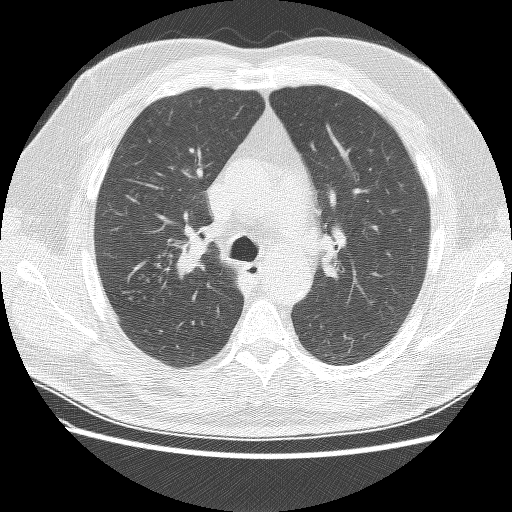
Chest CT (low-dose screening protocol), one axial image, first (baseline) screen, lung window (W 1500 / L -600 HU), 2.5 mm slice thickness, slice 62 of 159 in the series. Male, age 57 years at enrolment. Current smoker at enrolment.
- Expert reader's lesion annotation, bounding box [x1, y1, x2, y2] px = [158, 240, 213, 294].
- No non-calcified nodule or mass ≥4 mm was recorded by the screening reader at this exam.
- Official screen result: negative screen, minor abnormalities not suspicious for lung cancer.
- Lung cancer was diagnosed 434 days after this screen (after the second annual screen): non-small cell carcinoma, right upper lobe, poorly differentiated (G3), stage IIA (AJCC 6th edition), 25 mm at pathology.